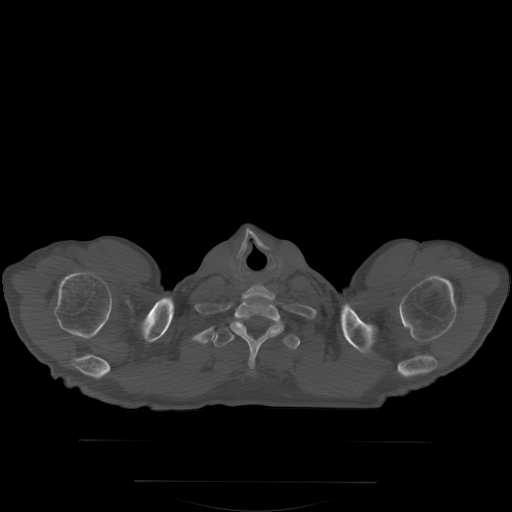
CT including the spine, one axial slice. Slice 294 of 350 in the series (ordered by position). Bone window (W 1800 / L 400 HU). 2.5 mm slice thickness. 512 × 512 image matrix, field of view 500 × 500 mm. Patient: male, 58 years. Case-level facts recorded for this patient, not image findings: primary cancer: prostate.
Annotated regions visible in this slice (semi-automatically segmented with operator editing):
- T1 vertebra: bounding box [x1, y1, x2, y2] px = [231, 321, 298, 348]